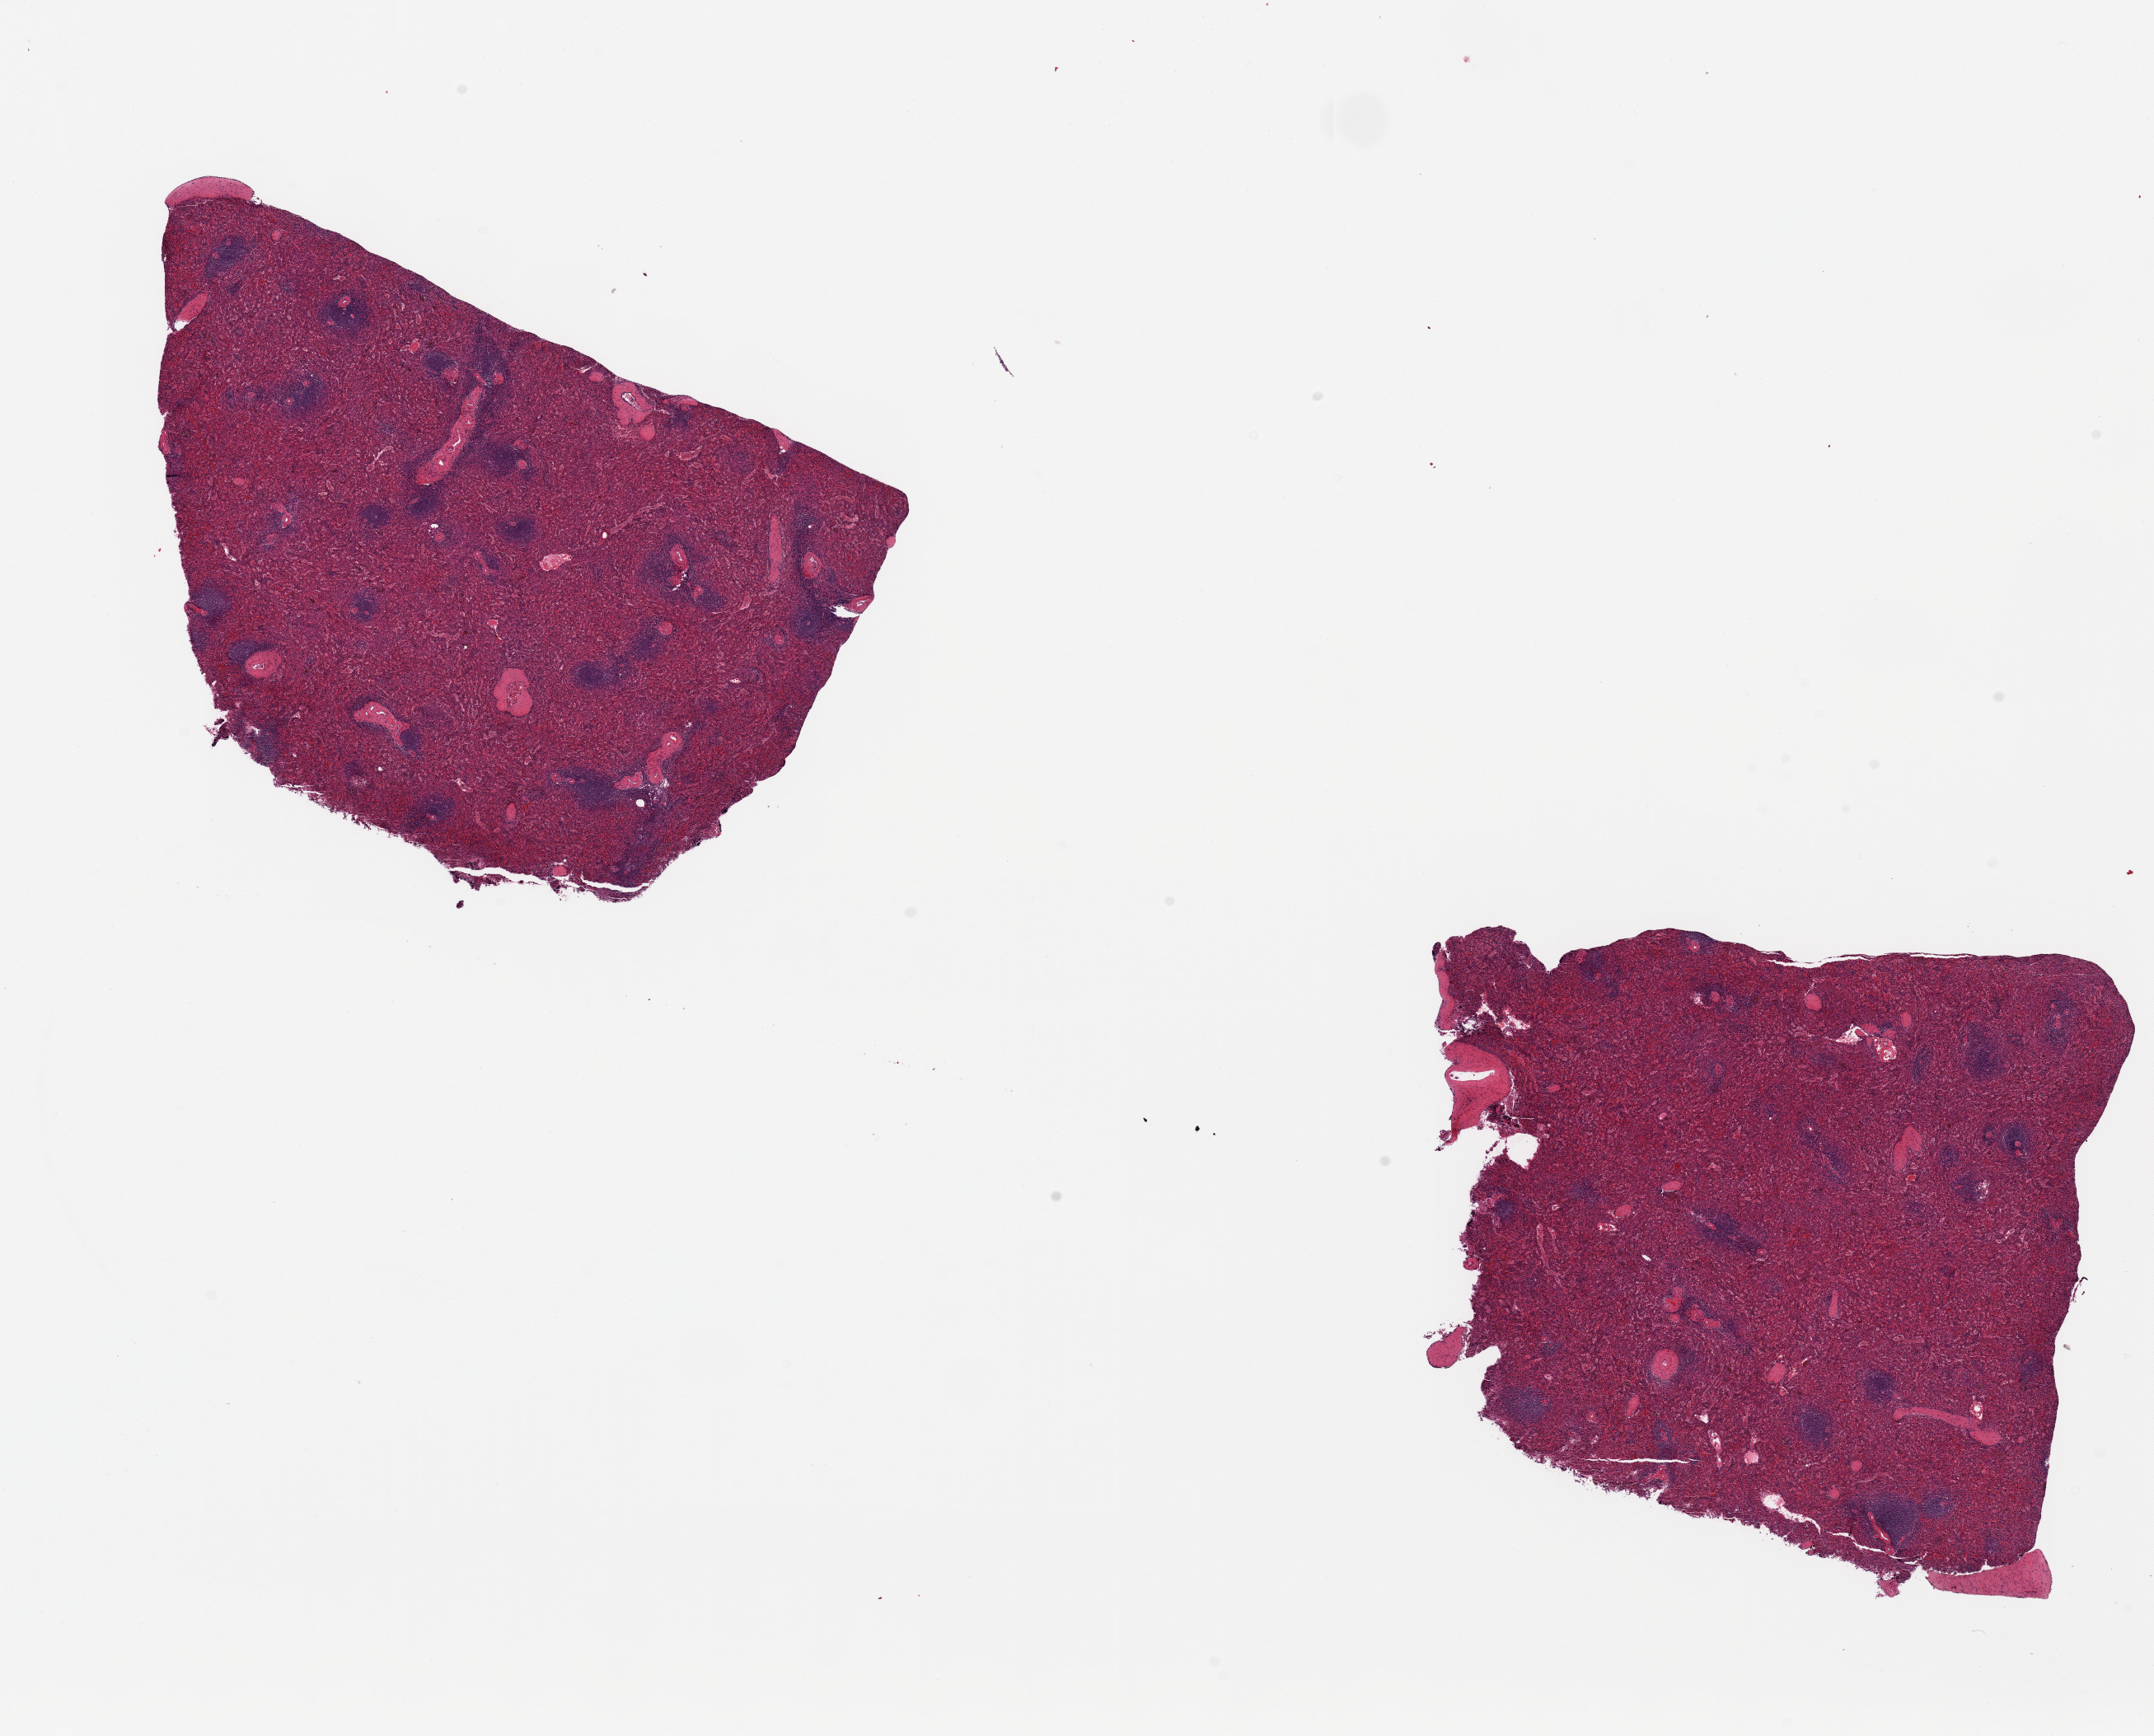
Whole-slide image, H&E stain, brightfield, whole scanned area (about 20.7 x 16.7 mm, from a 20x scan) shown as a low-resolution overview, PAXgene-fixed paraffin-embedded (PFPE) section, section of spleen (target tissue), tissue donor sample. Donor sex: male.
Pathologist's review note for this sample: 2 ~7x6.5mm pieces, focally under-fixed, with holes/tears.